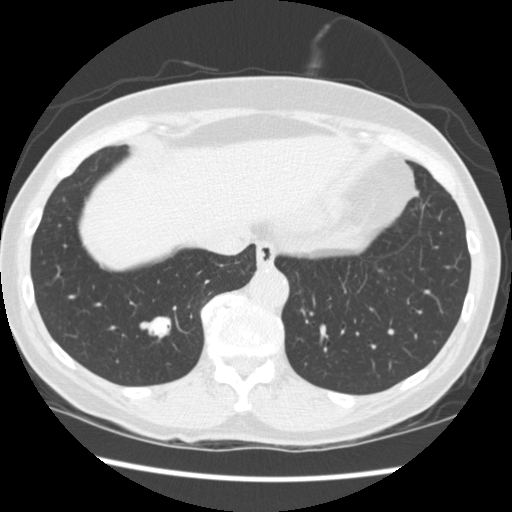
Low-dose screening chest CT, one axial slice; position 65 of 262 along the scan axis; lung window (W 1500 / L -600 HU); 2.5 mm slice thickness; 512 × 512 image matrix, field of view 340 × 340 mm.
Annotated regions visible in this slice (manually delineated by an expert):
- lesion 1 (tumor, lower lobe of right lung): bounding box (x1, y1, x2, y2) in pixels: (148, 317, 171, 338)